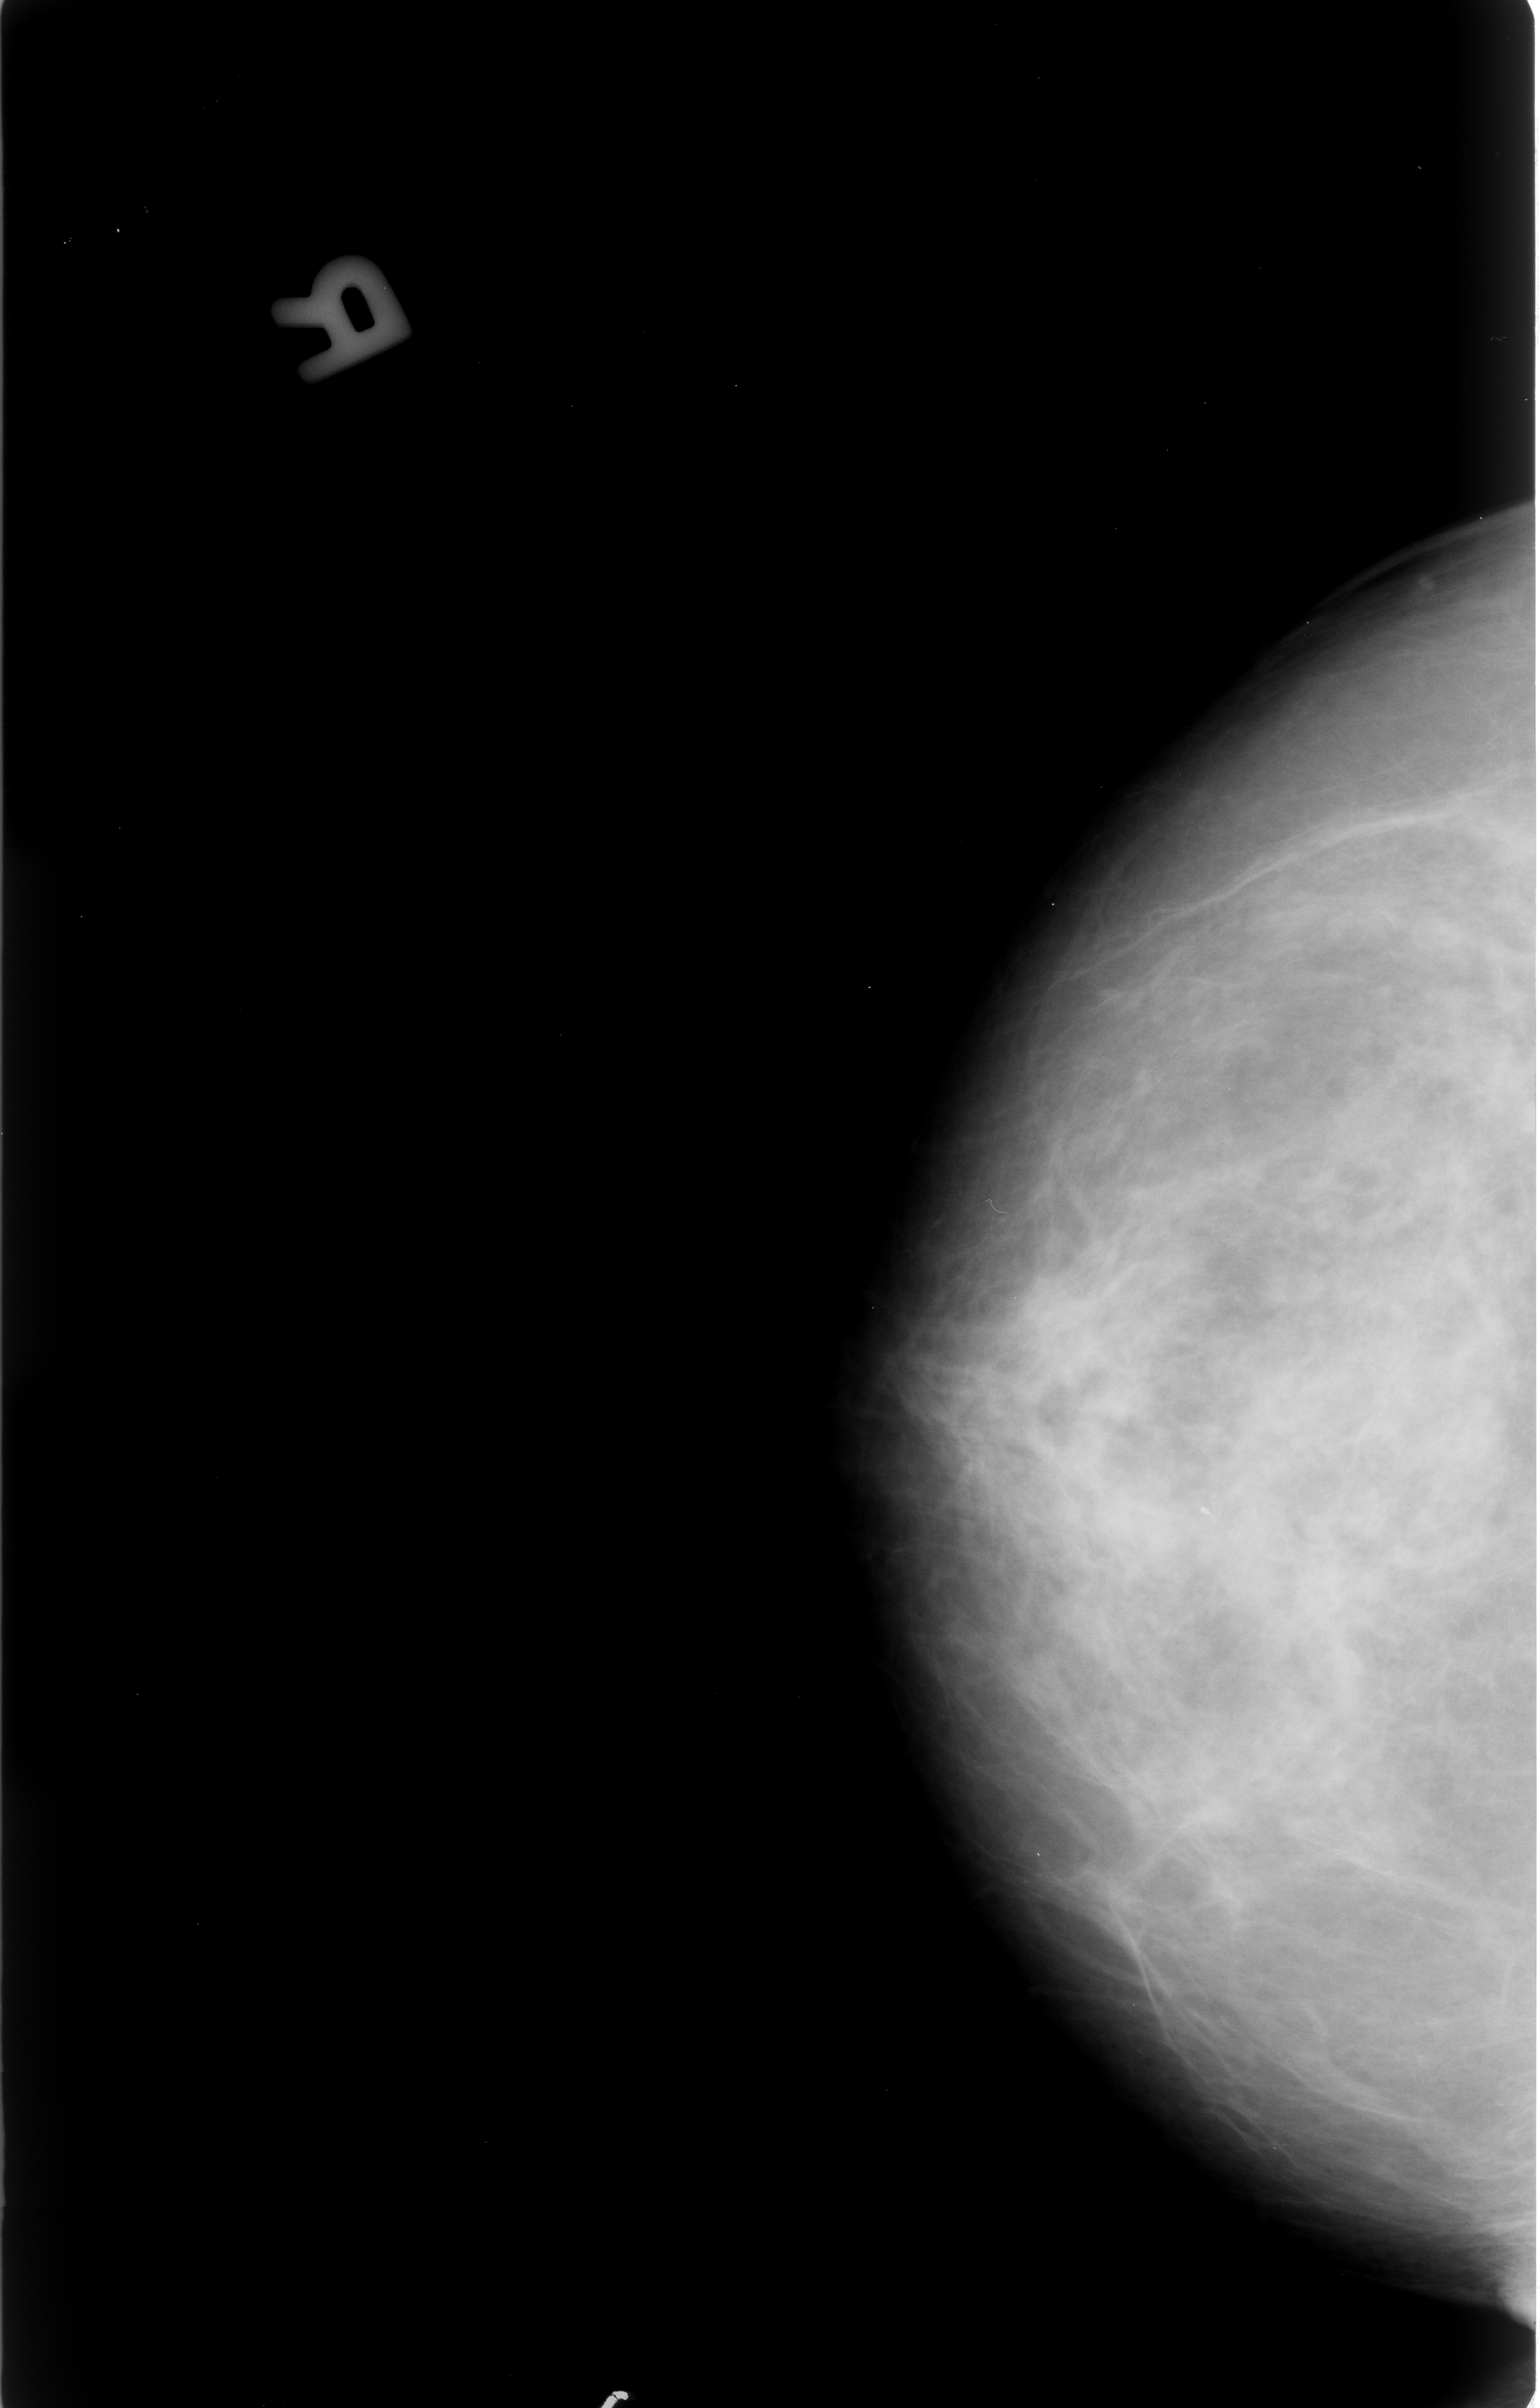
Mammogram (digitized film), right breast, CC view, BI-RADS breast density category 2 (scale 1–4).
Marked findings (only marked abnormalities are described; nothing is implied about the rest of the image): calcifications, morphology punctate, distribution clustered; BI-RADS assessment category 3; pathology result (as recorded, not read from the image): malignant.